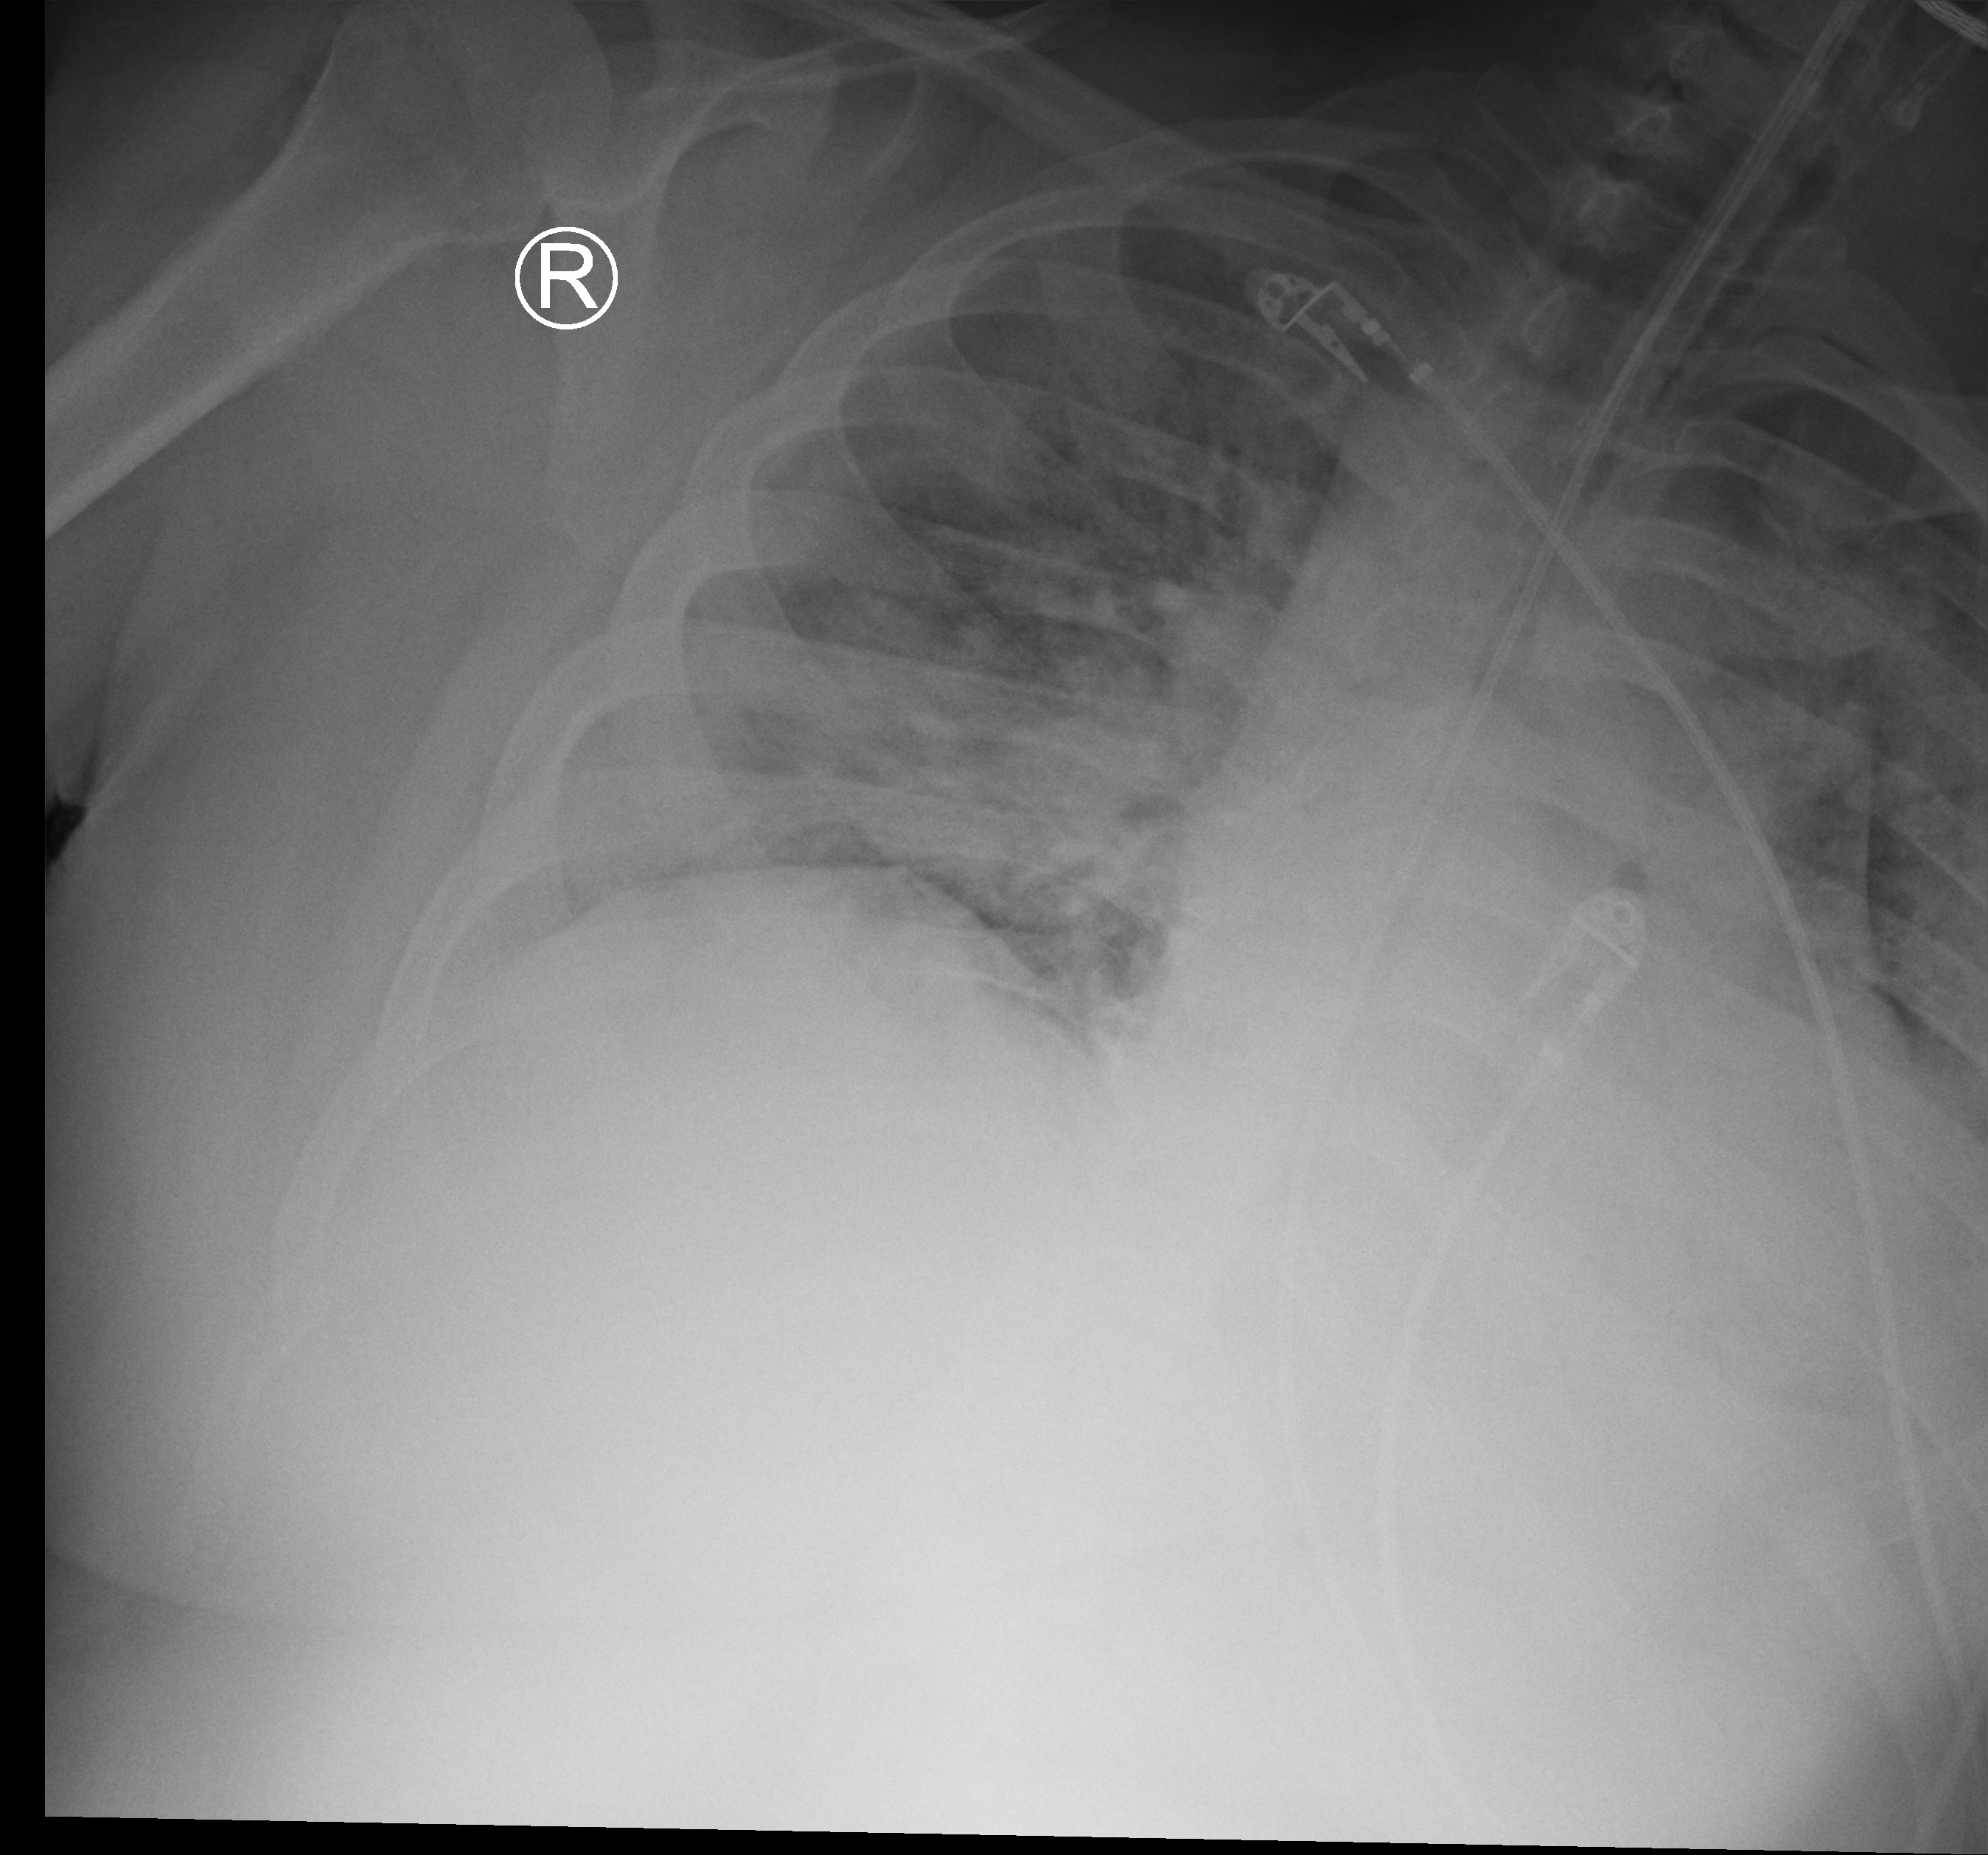
Portable chest radiograph; anteroposterior (AP) projection. Patient hospitalised with COVID-19, aged 18–59 years.
Admission-level facts for this patient (not findings on this image; timing relative to this image not recorded): mechanically ventilated during this hospital stay: yes; admitted to intensive care during this hospital stay: yes.